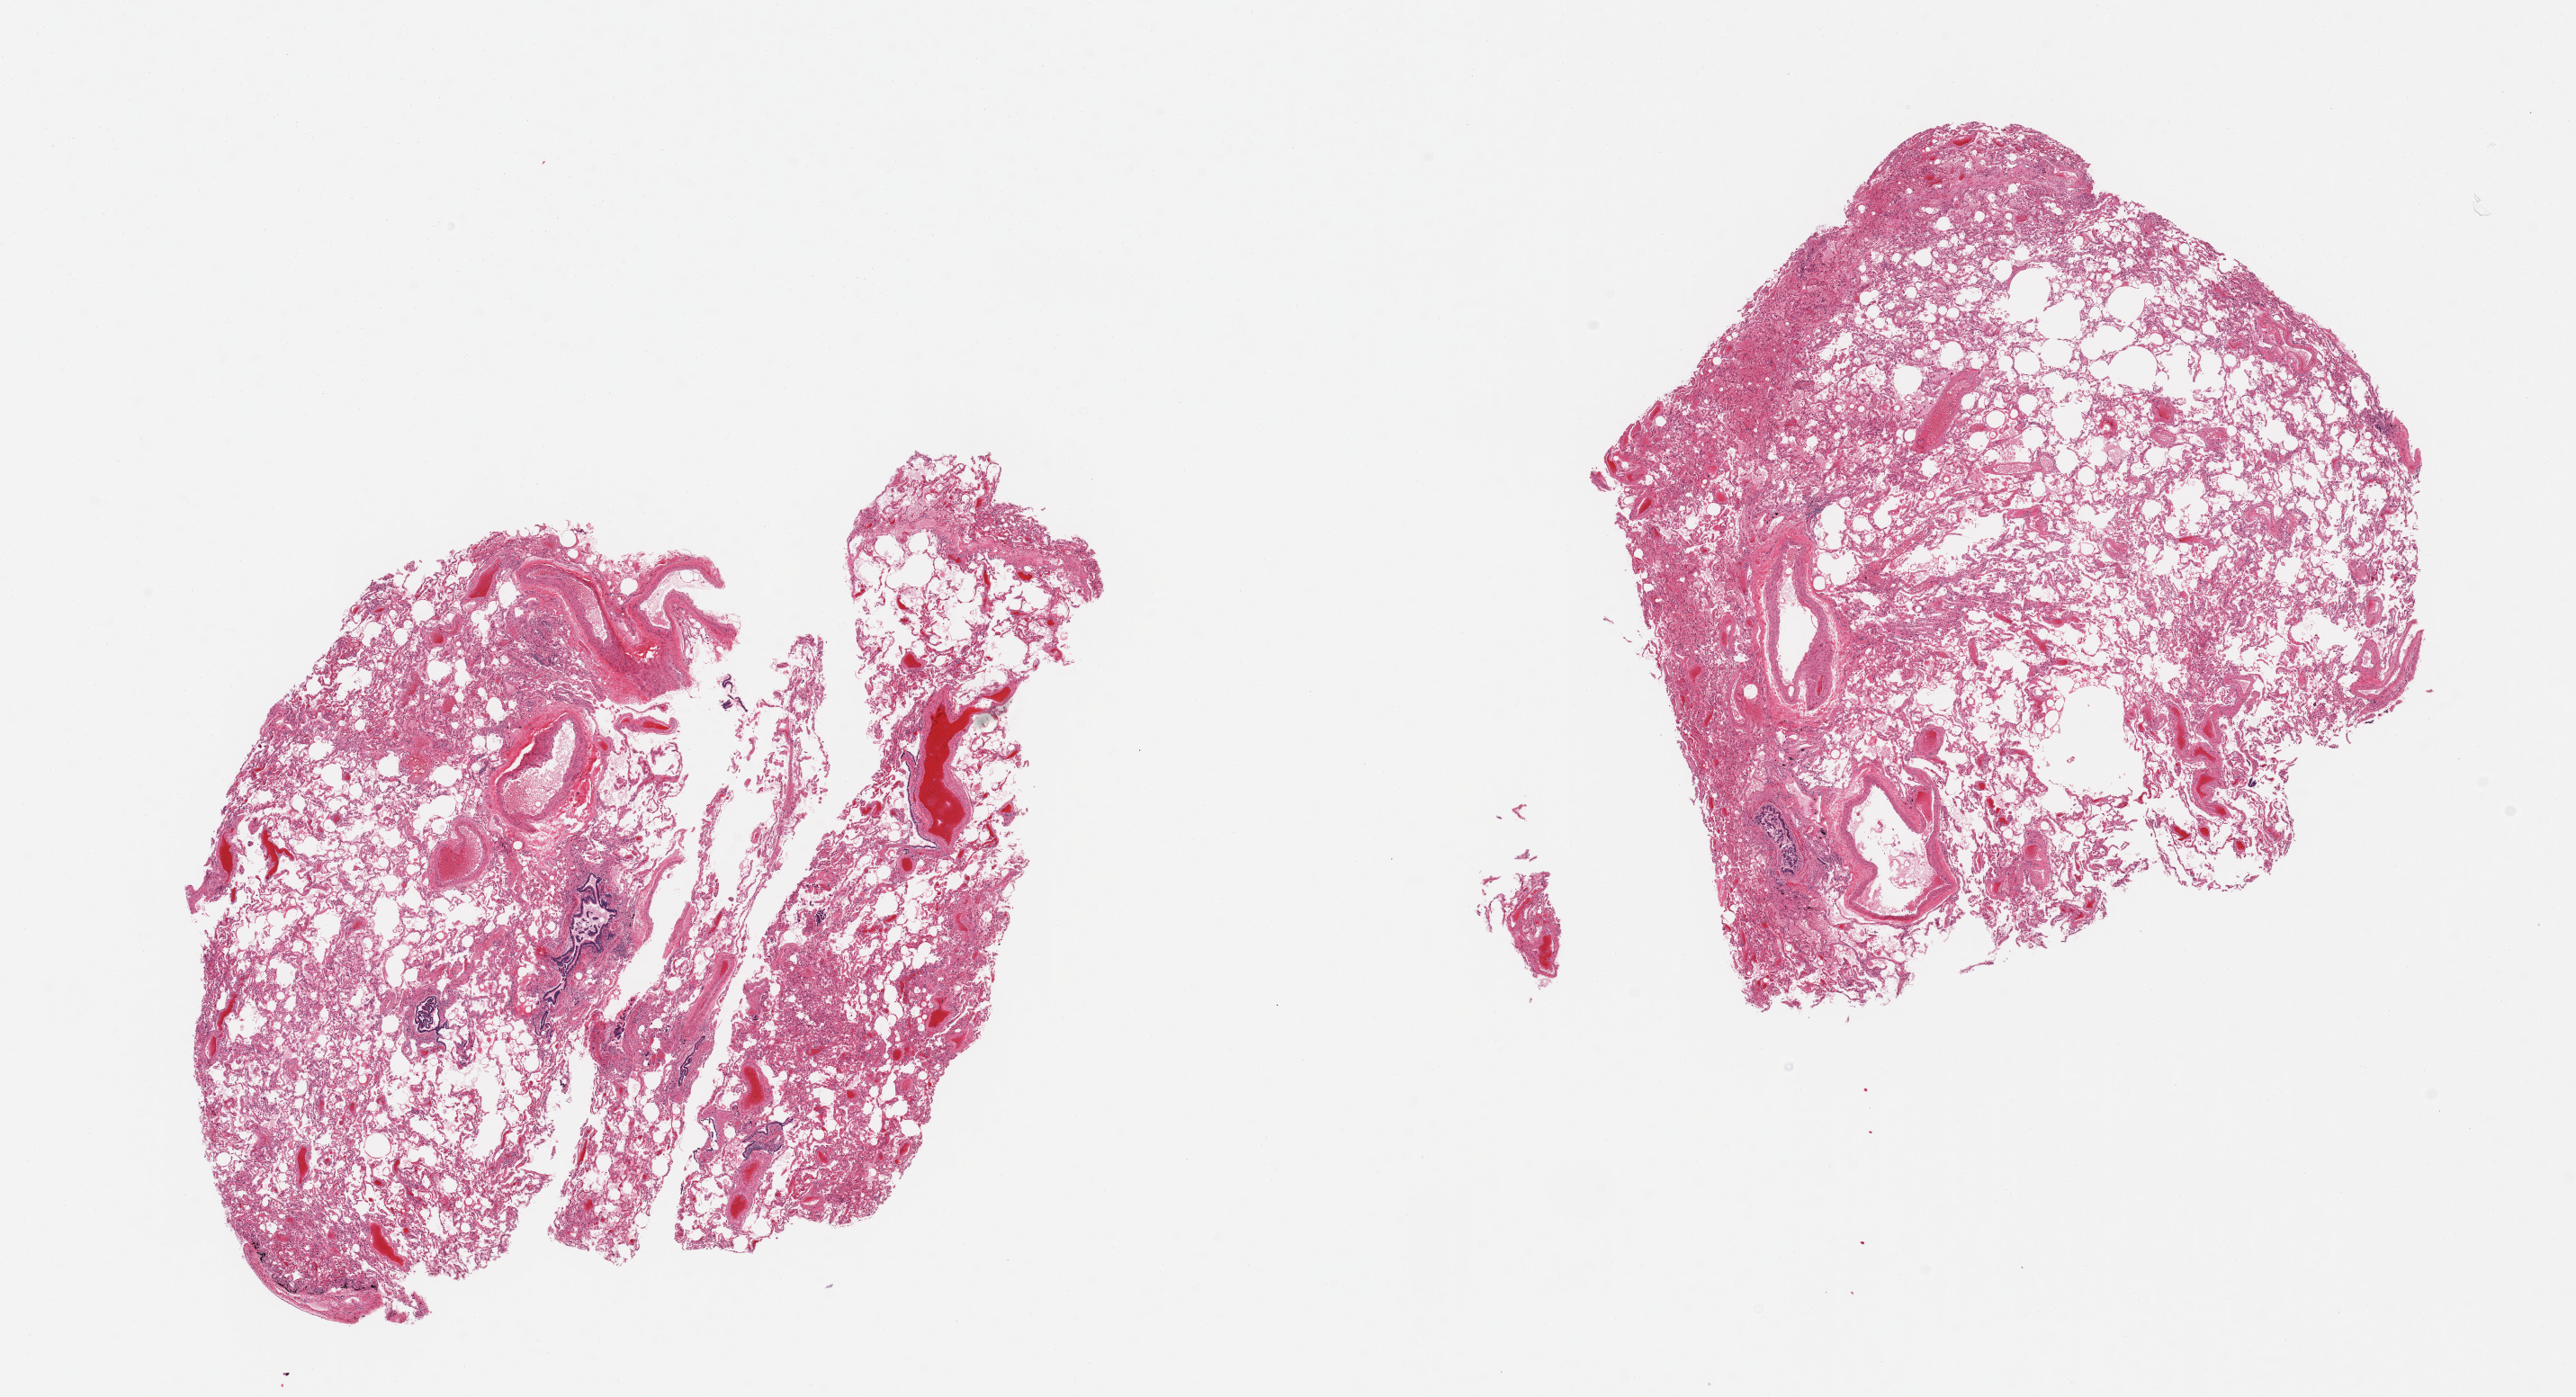
Haematoxylin and eosin whole-slide image, brightfield — shown as a low-resolution overview of the whole scanned area (about 22.6 x 12.3 mm, from a 20x scan). PAXgene-fixed paraffin-embedded (PFPE) section. Target tissue: lung. Donor tissue sample. Donor sex: male.
* review note (as recorded): 2 pieces, moderate congestion